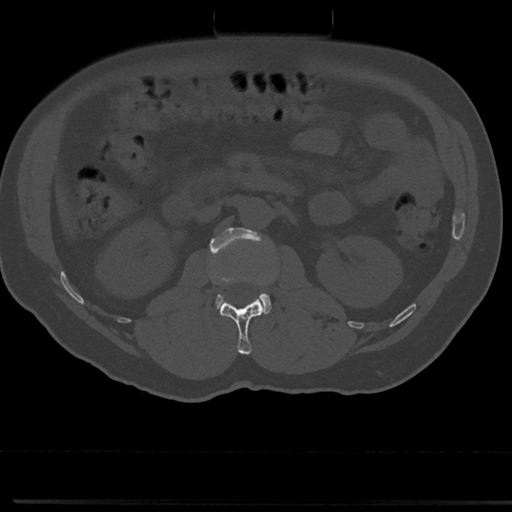
CT including the spine, one axial slice; position 49 of 817 along the scan axis; bone window (W 1800 / L 400 HU); 512 × 512 image matrix. Male patient, age 61 years. Case-level facts recorded for this patient, not image findings: primary cancer: prostate.
Structures marked on this image (semi-automatically segmented with operator editing):
- L1 vertebra: bounding box (x1, y1, x2, y2) in pixels: (219, 298, 264, 355)
- L2 vertebra: (209, 227, 271, 314)